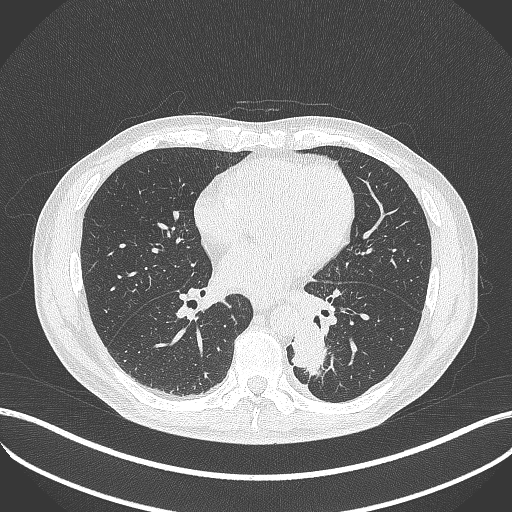
Chest CT, one axial slice; slice 177 of 451 in the series (ordered by position); reconstruction kernel B70f; 120 kVp; lung window (W 1500 / L -600 HU); 1 mm slice thickness; 512 × 512 image matrix. Patient: male, 72 years. Case-level facts recorded for this patient, not image findings: clinical TNM (as recorded): T2b N0 M1.
Structures marked on this image (bounding box drawn by a radiologist):
- lung tumour (recorded histology: adenocarcinoma): box from (x=286, y=313) to (x=333, y=379) px